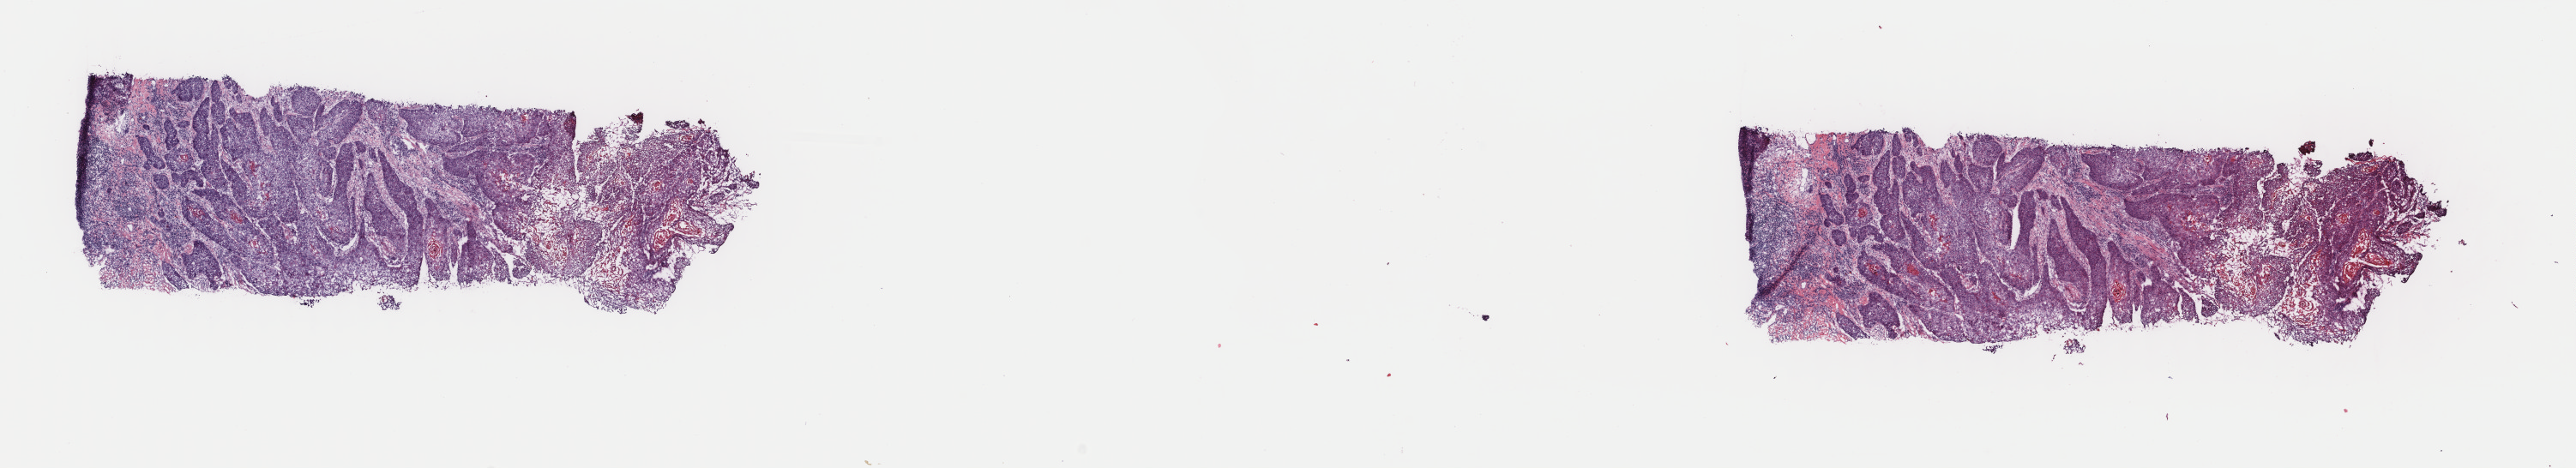
Whole-slide histology image, H&E, low-resolution overview of the scanned area, about 23.8 x 4.3 mm (slide scanned at 40x); frozen section; primary tumour sample from the head and neck. Patient: male, age at initial diagnosis 53 years. Histologic grade: G2 (moderately differentiated). Slide review estimates, as recorded: tumour cells 100%, tumour nuclei 65%, normal cells 0%, stromal cells 0%, necrosis 0%. Infiltration values recorded for this section: lymphocyte infiltration 10%, monocyte infiltration 0%, neutrophil infiltration 2%.
* diagnosis: Squamous cell carcinoma, NOS (base of tongue, NOS)